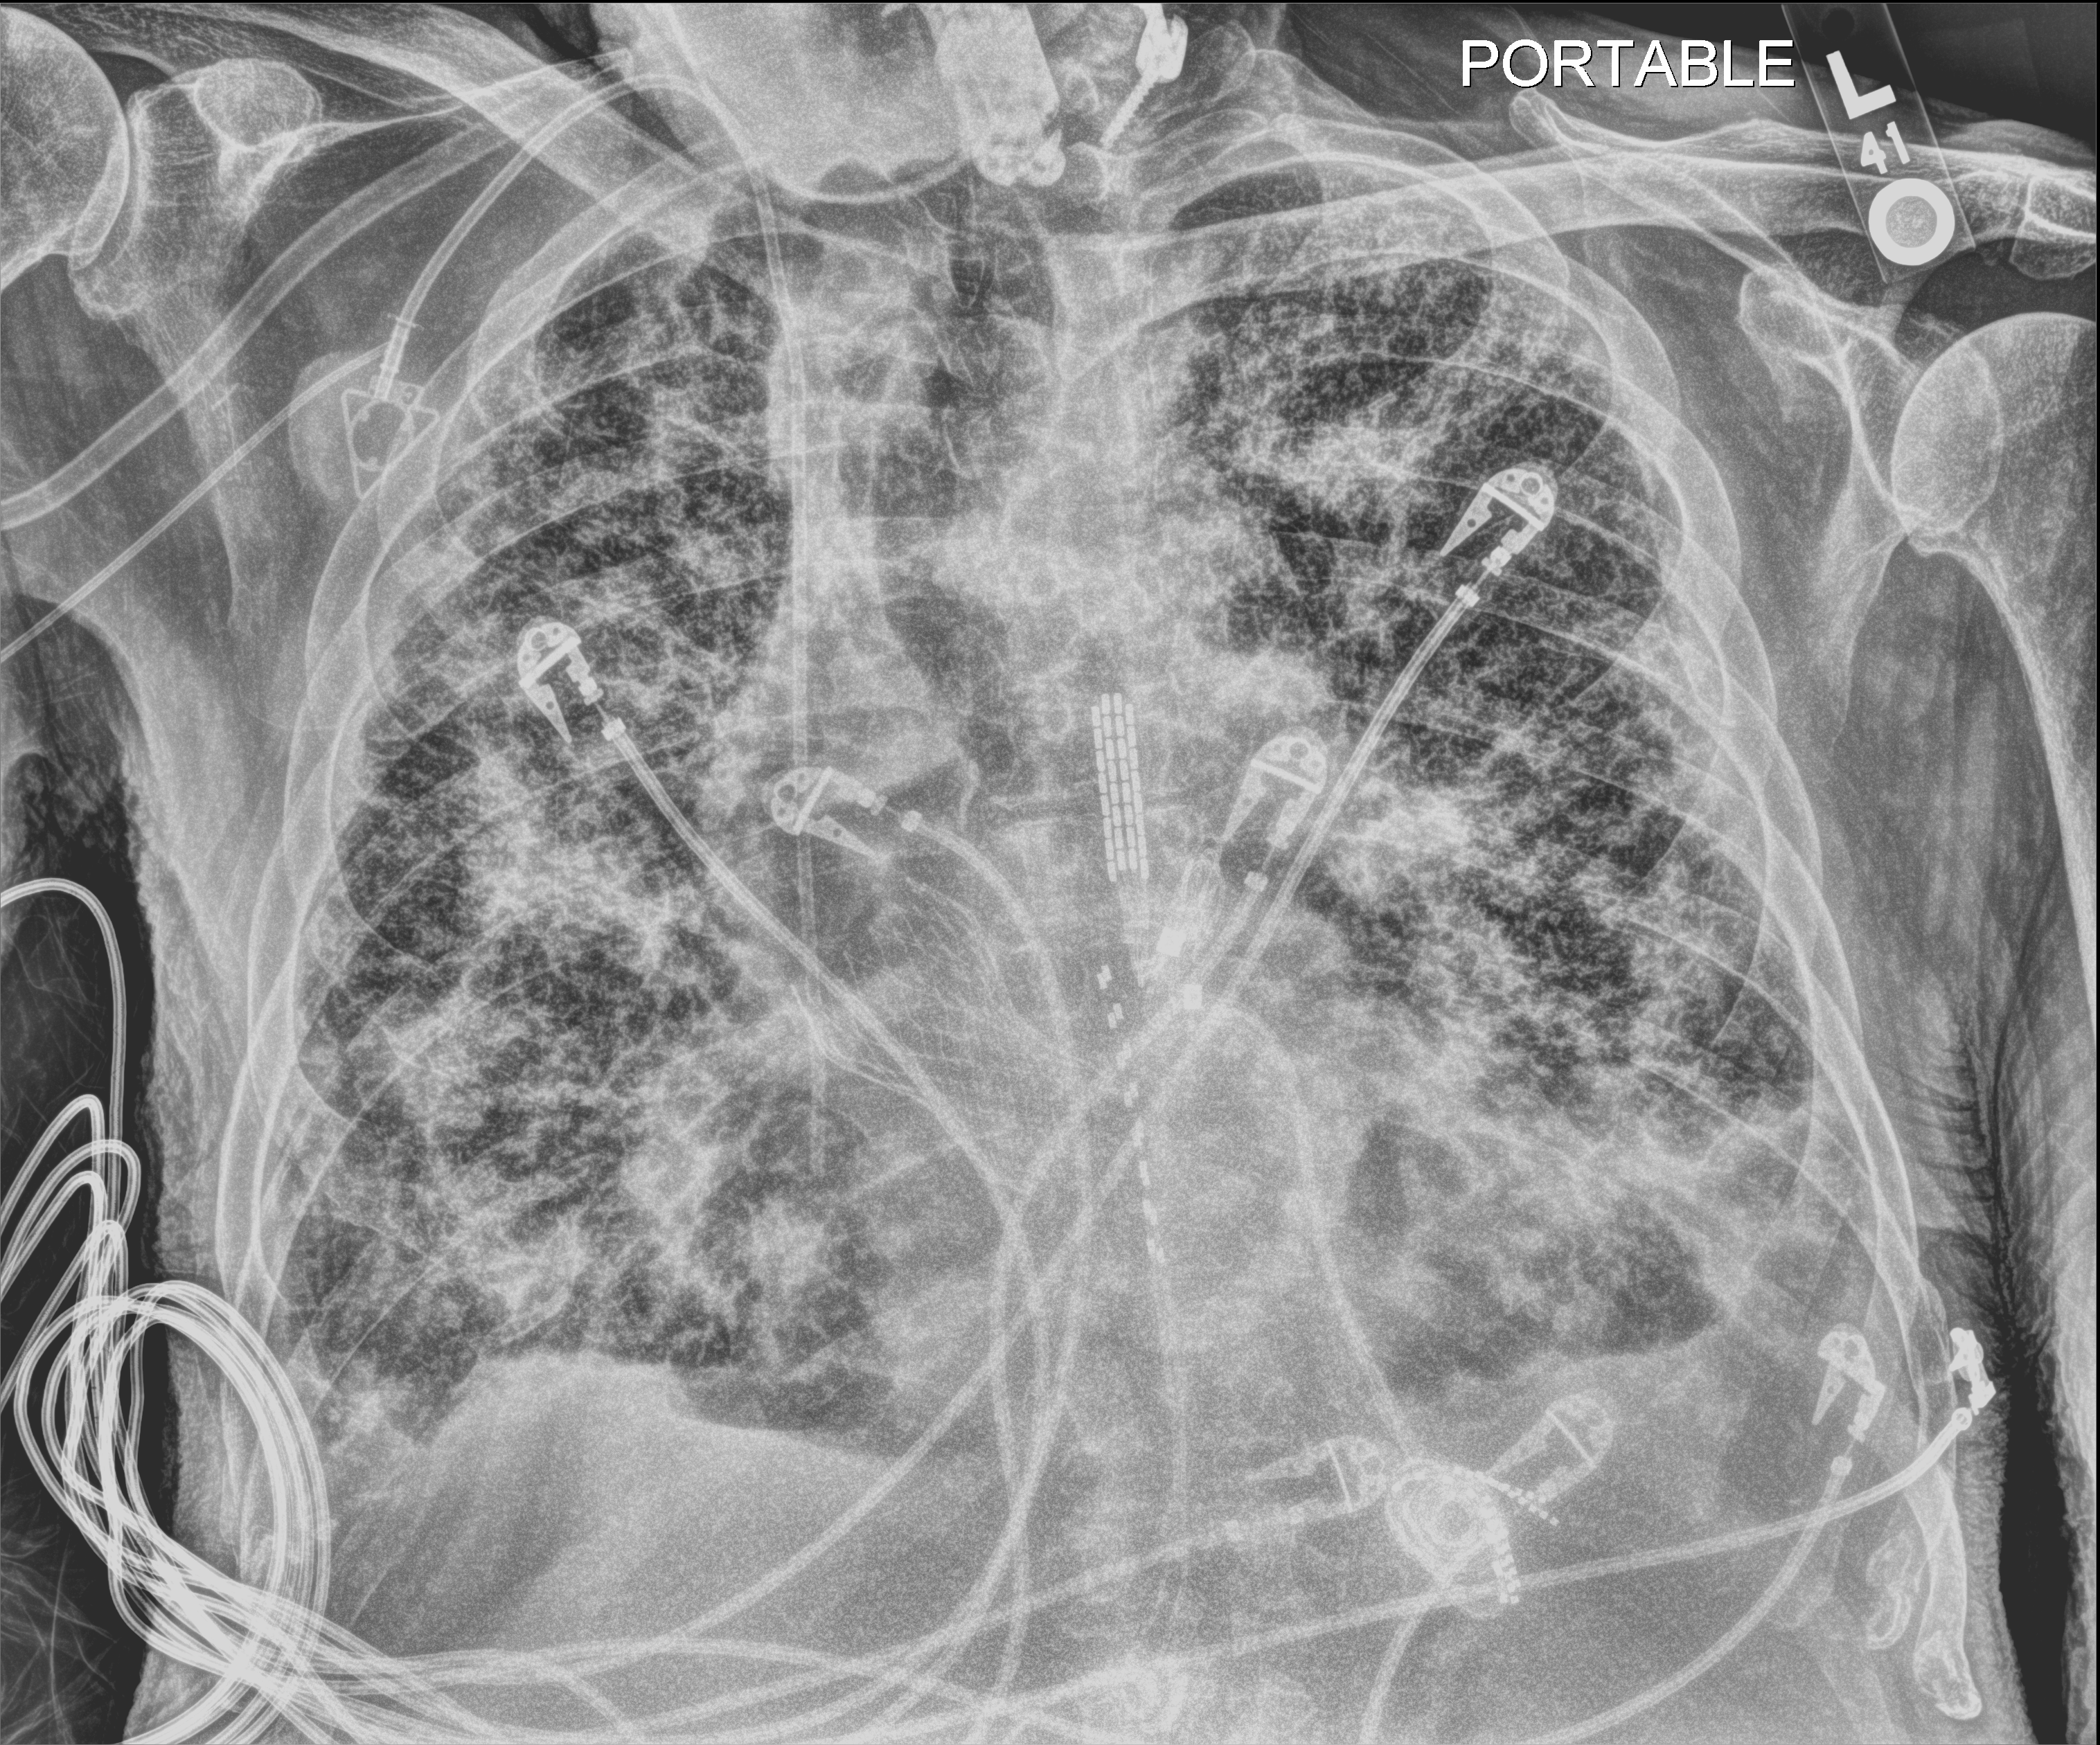
Chest X-ray (portable). Patient hospitalised with COVID-19; male, aged 75–90 years.
Admission-level facts for this patient (not findings on this image; timing relative to this image not recorded): mechanically ventilated during this hospital stay: no; admitted to intensive care during this hospital stay: yes.